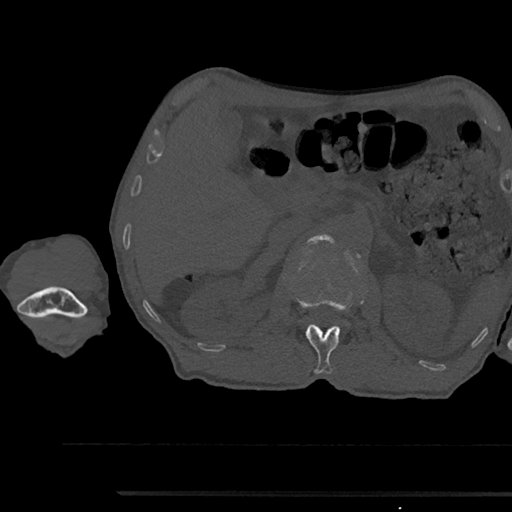
CT including the spine, one axial slice; position 617 of 797 along the scan axis; 120 kVp; bone window (W 1800 / L 400 HU); 0.5 mm slice thickness; 512 × 512 image matrix, field of view 367 × 367 mm. Male patient, age 79 years. From the clinical record (not read from this slice): primary cancer: prostate.
Annotated regions visible in this slice (semi-automatically segmented with operator editing):
- L1 vertebra: bounding box <294,295,346,374> (left, top, right, bottom; pixels)
- L2 vertebra: <308,234,335,244>